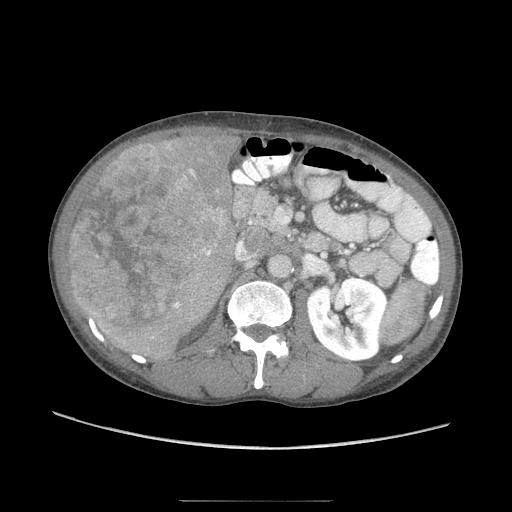
Contrast-enhanced abdominal CT (liver protocol), one axial slice; slice 32 of 103 in the series (ordered by position); reconstruction kernel STANDARD; 120 kVp; soft-tissue window (W 400 / L 40 HU); 2.5 mm slice thickness; 512 × 512 image matrix, field of view 380 × 380 mm. From the clinical record (not read from this slice): diagnosis: hepatocellular carcinoma (patient treated with transarterial chemoembolisation; whether this scan precedes or follows treatment is not stated here); TNM stage (as recorded): Stage-IIIA; Child-Pugh class: A; tumour differentiation: moderately differentiated; tumour nodularity: multinodular.
Structures marked on this image (semi-automatic segmentation, software-assisted and operator-edited):
- liver parenchyma outside the tumour (the mass and vessels are separate outlines, so this box may not span the whole liver): box from (x=70, y=136) to (x=240, y=354) px
- mass: (x=66, y=140)–(x=220, y=344)